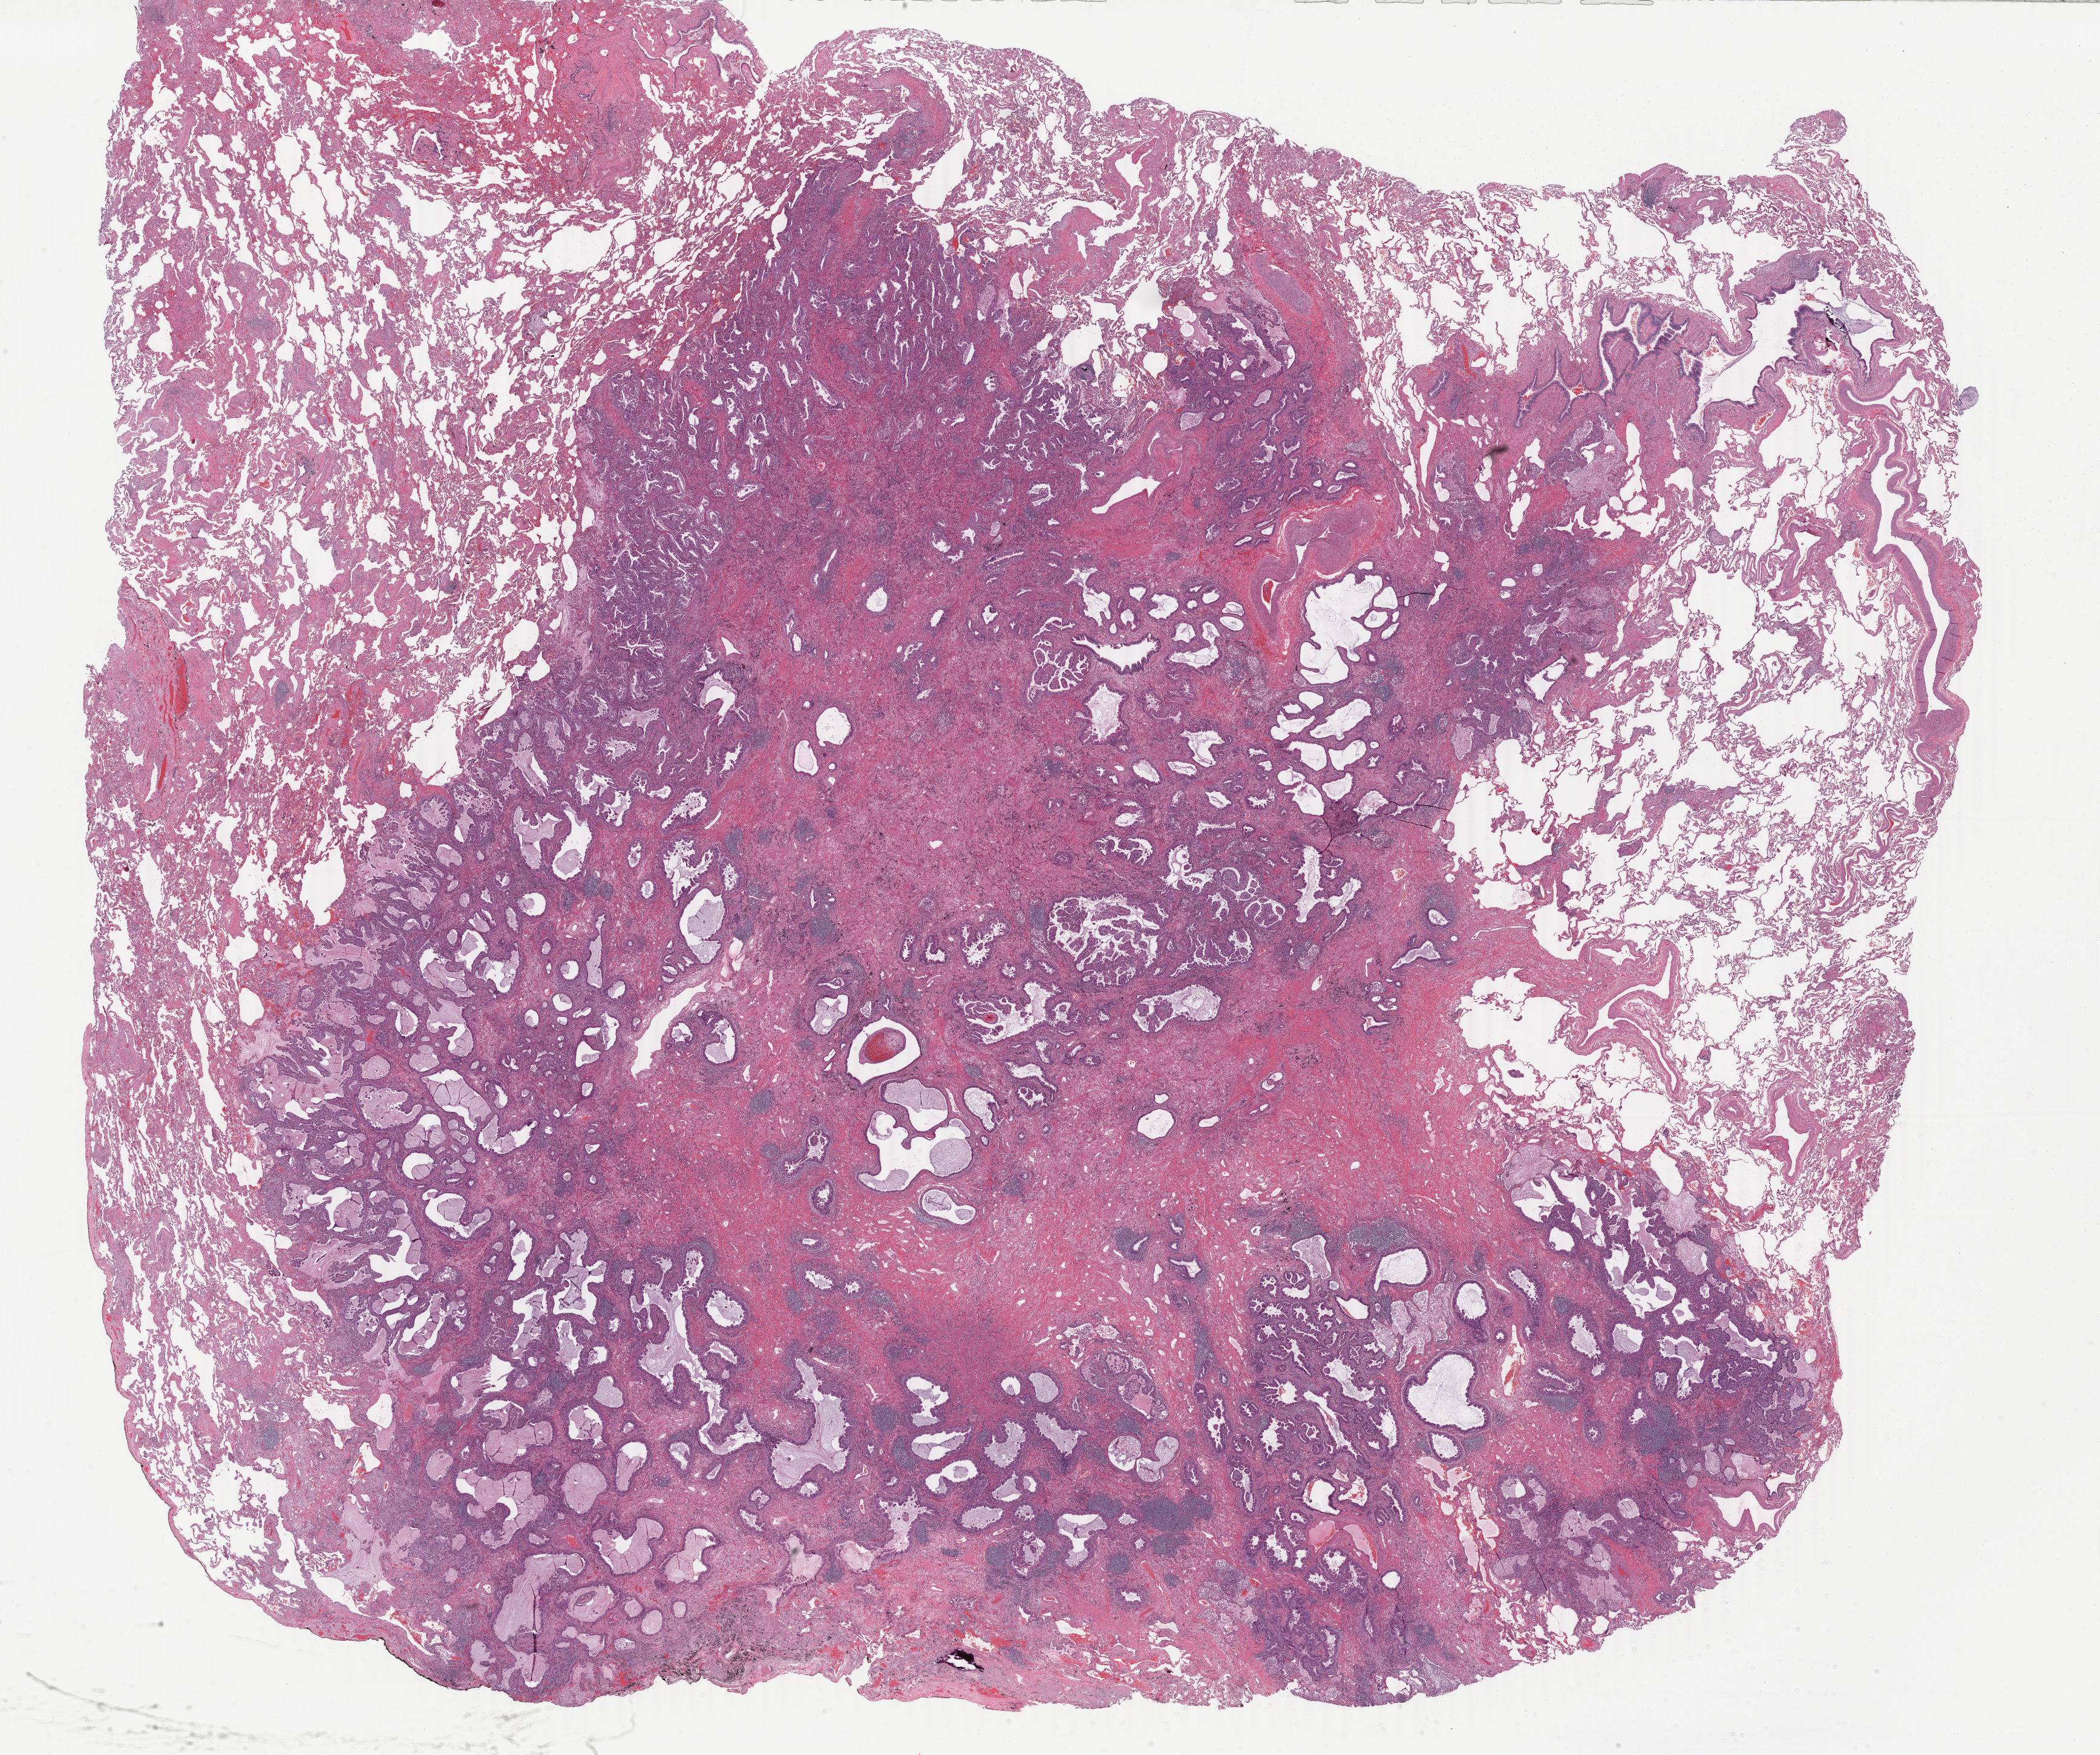
Whole-slide histology image, H&E — low-resolution overview of the scanned area, about 27.6 x 23.1 mm (slide scanned at 40x); formalin-fixed paraffin-embedded (FFPE) diagnostic section; lung, primary tumour sample. Male, age 83 years at initial diagnosis.
* diagnosis: Adenocarcinoma with mixed subtypes (upper lobe, lung)
* AJCC pathologic stage: IA (7th edition)